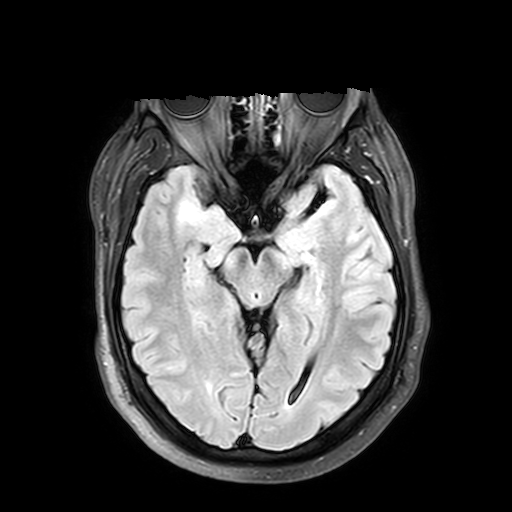
Brain MRI from a brain-tumour surgery series, one axial slice. Slice 25 of 42 in the series (ordered by position). T2 FLAIR. 4 mm slice thickness. 512 × 512 image matrix. From the clinical record (not read from this slice): histopathology: Astrocytoma; WHO grade: 2; IDH mutation: yes; tumour location: Right Insular.
Annotated regions visible in this slice (expert manual segmentation):
- tumour: box from (x=140, y=200) to (x=157, y=223) px